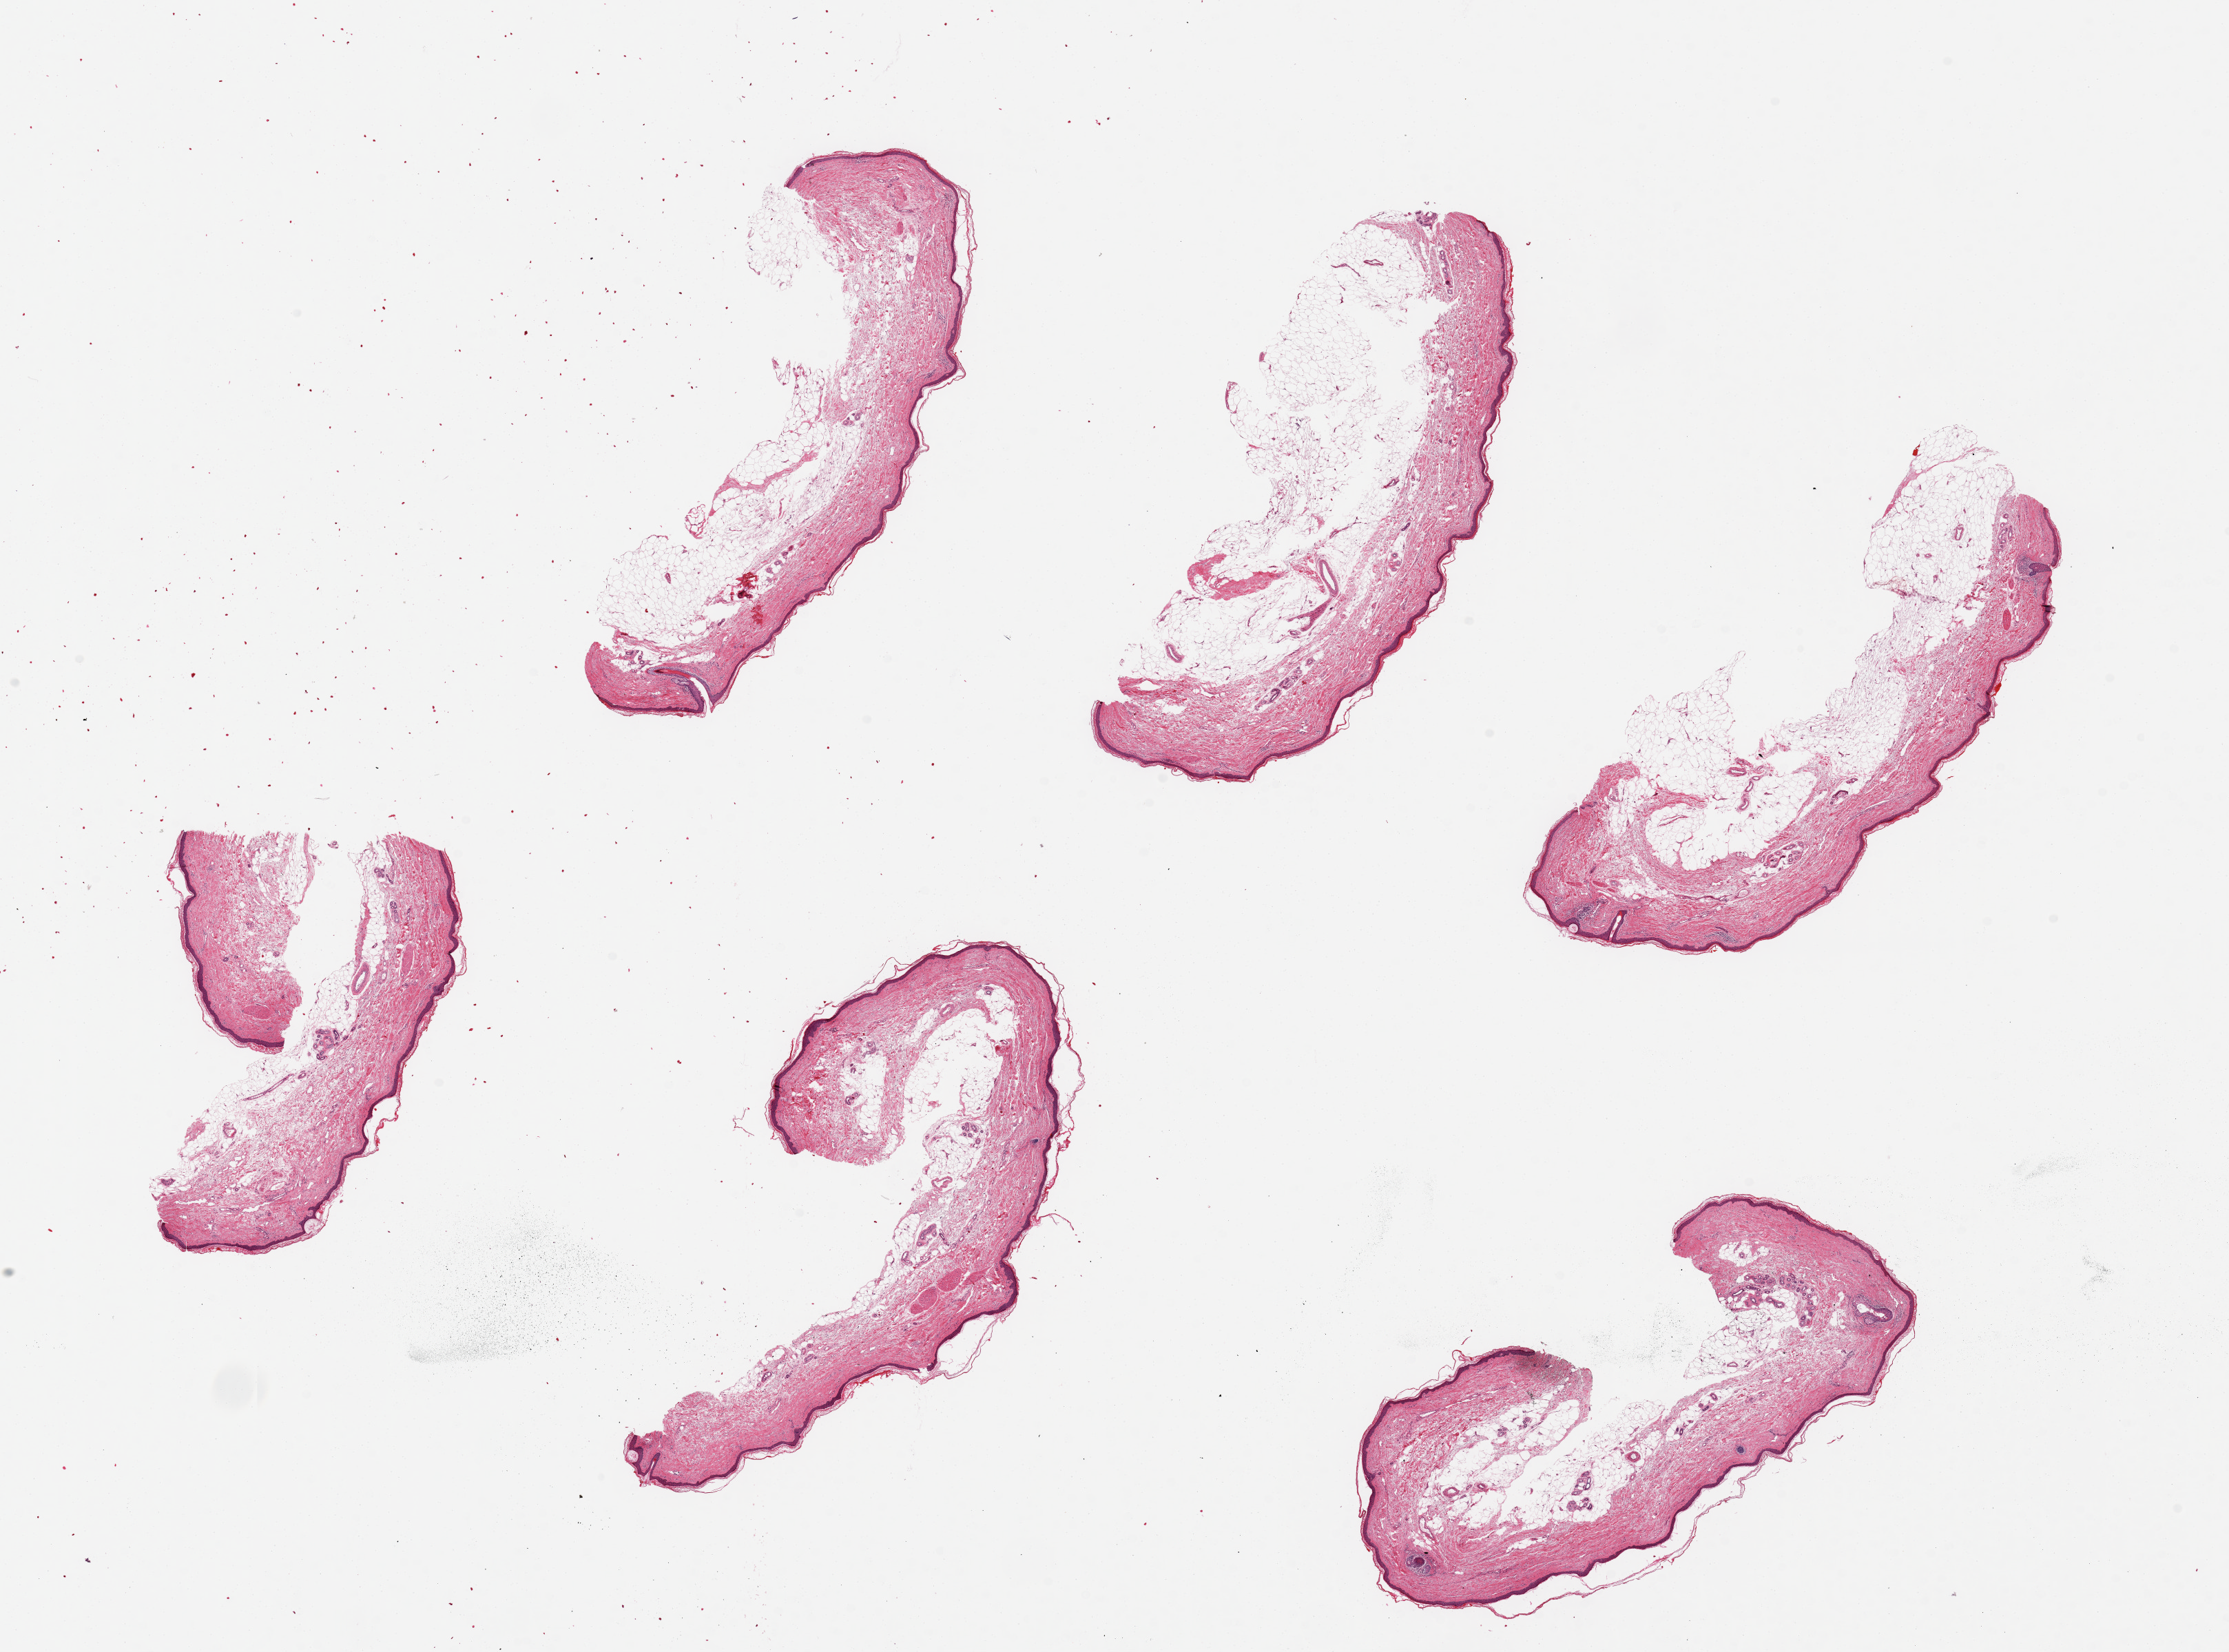
Whole-slide image, haematoxylin and eosin stain — shown as a low-resolution overview of the whole scanned area (about 25.6 x 19.0 mm, acquisition: 20x scan), PAXgene-fixed paraffin-embedded (PFPE) section, target tissue: skin of lower leg, donor tissue sample. Male donor.
Pathologist's review note for this sample: 6 pieces ~7x2.5mm. Squamous epithelium is ~2-3% of thickness.